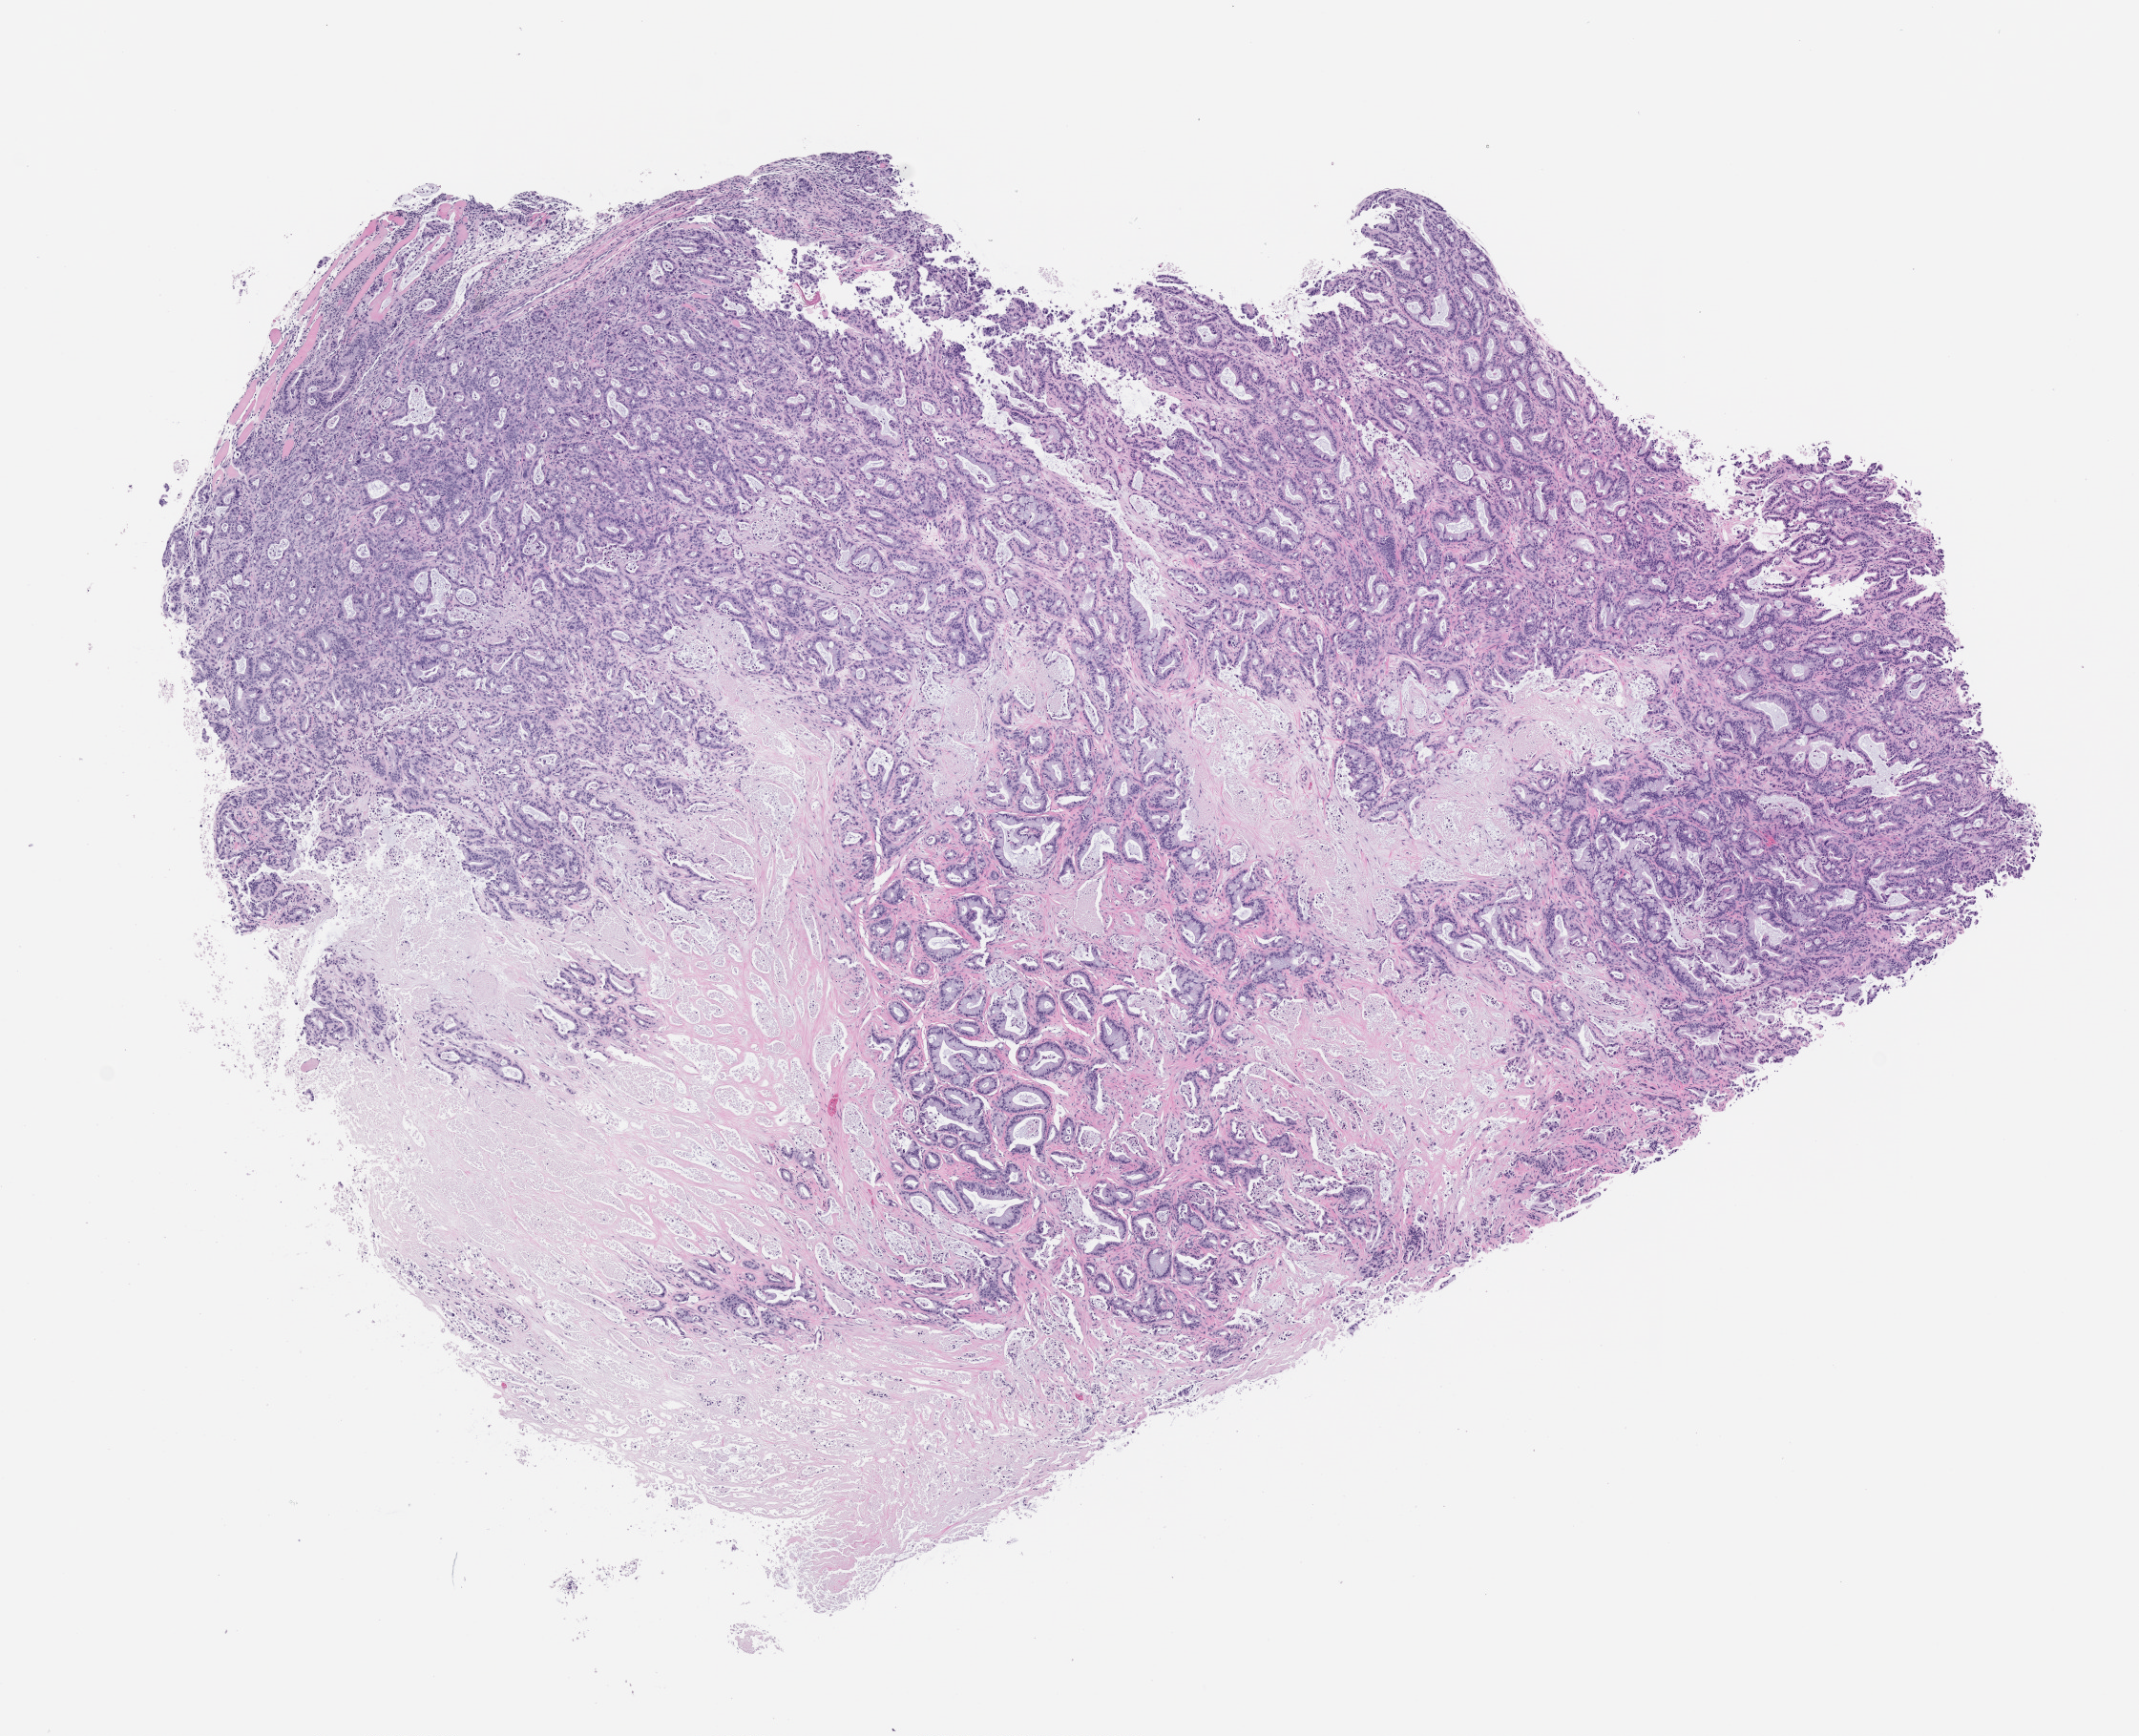
Whole-slide image, haematoxylin and eosin: patient-derived xenograft (human tumor grown in a mouse), passage 5 — low-resolution overview of the scanned area, about 9.0 x 7.3 mm; formalin-fixed paraffin-embedded section; tumor site category: pancreas.
Originating patient diagnosis: Pancreatic Adenocarcinoma.